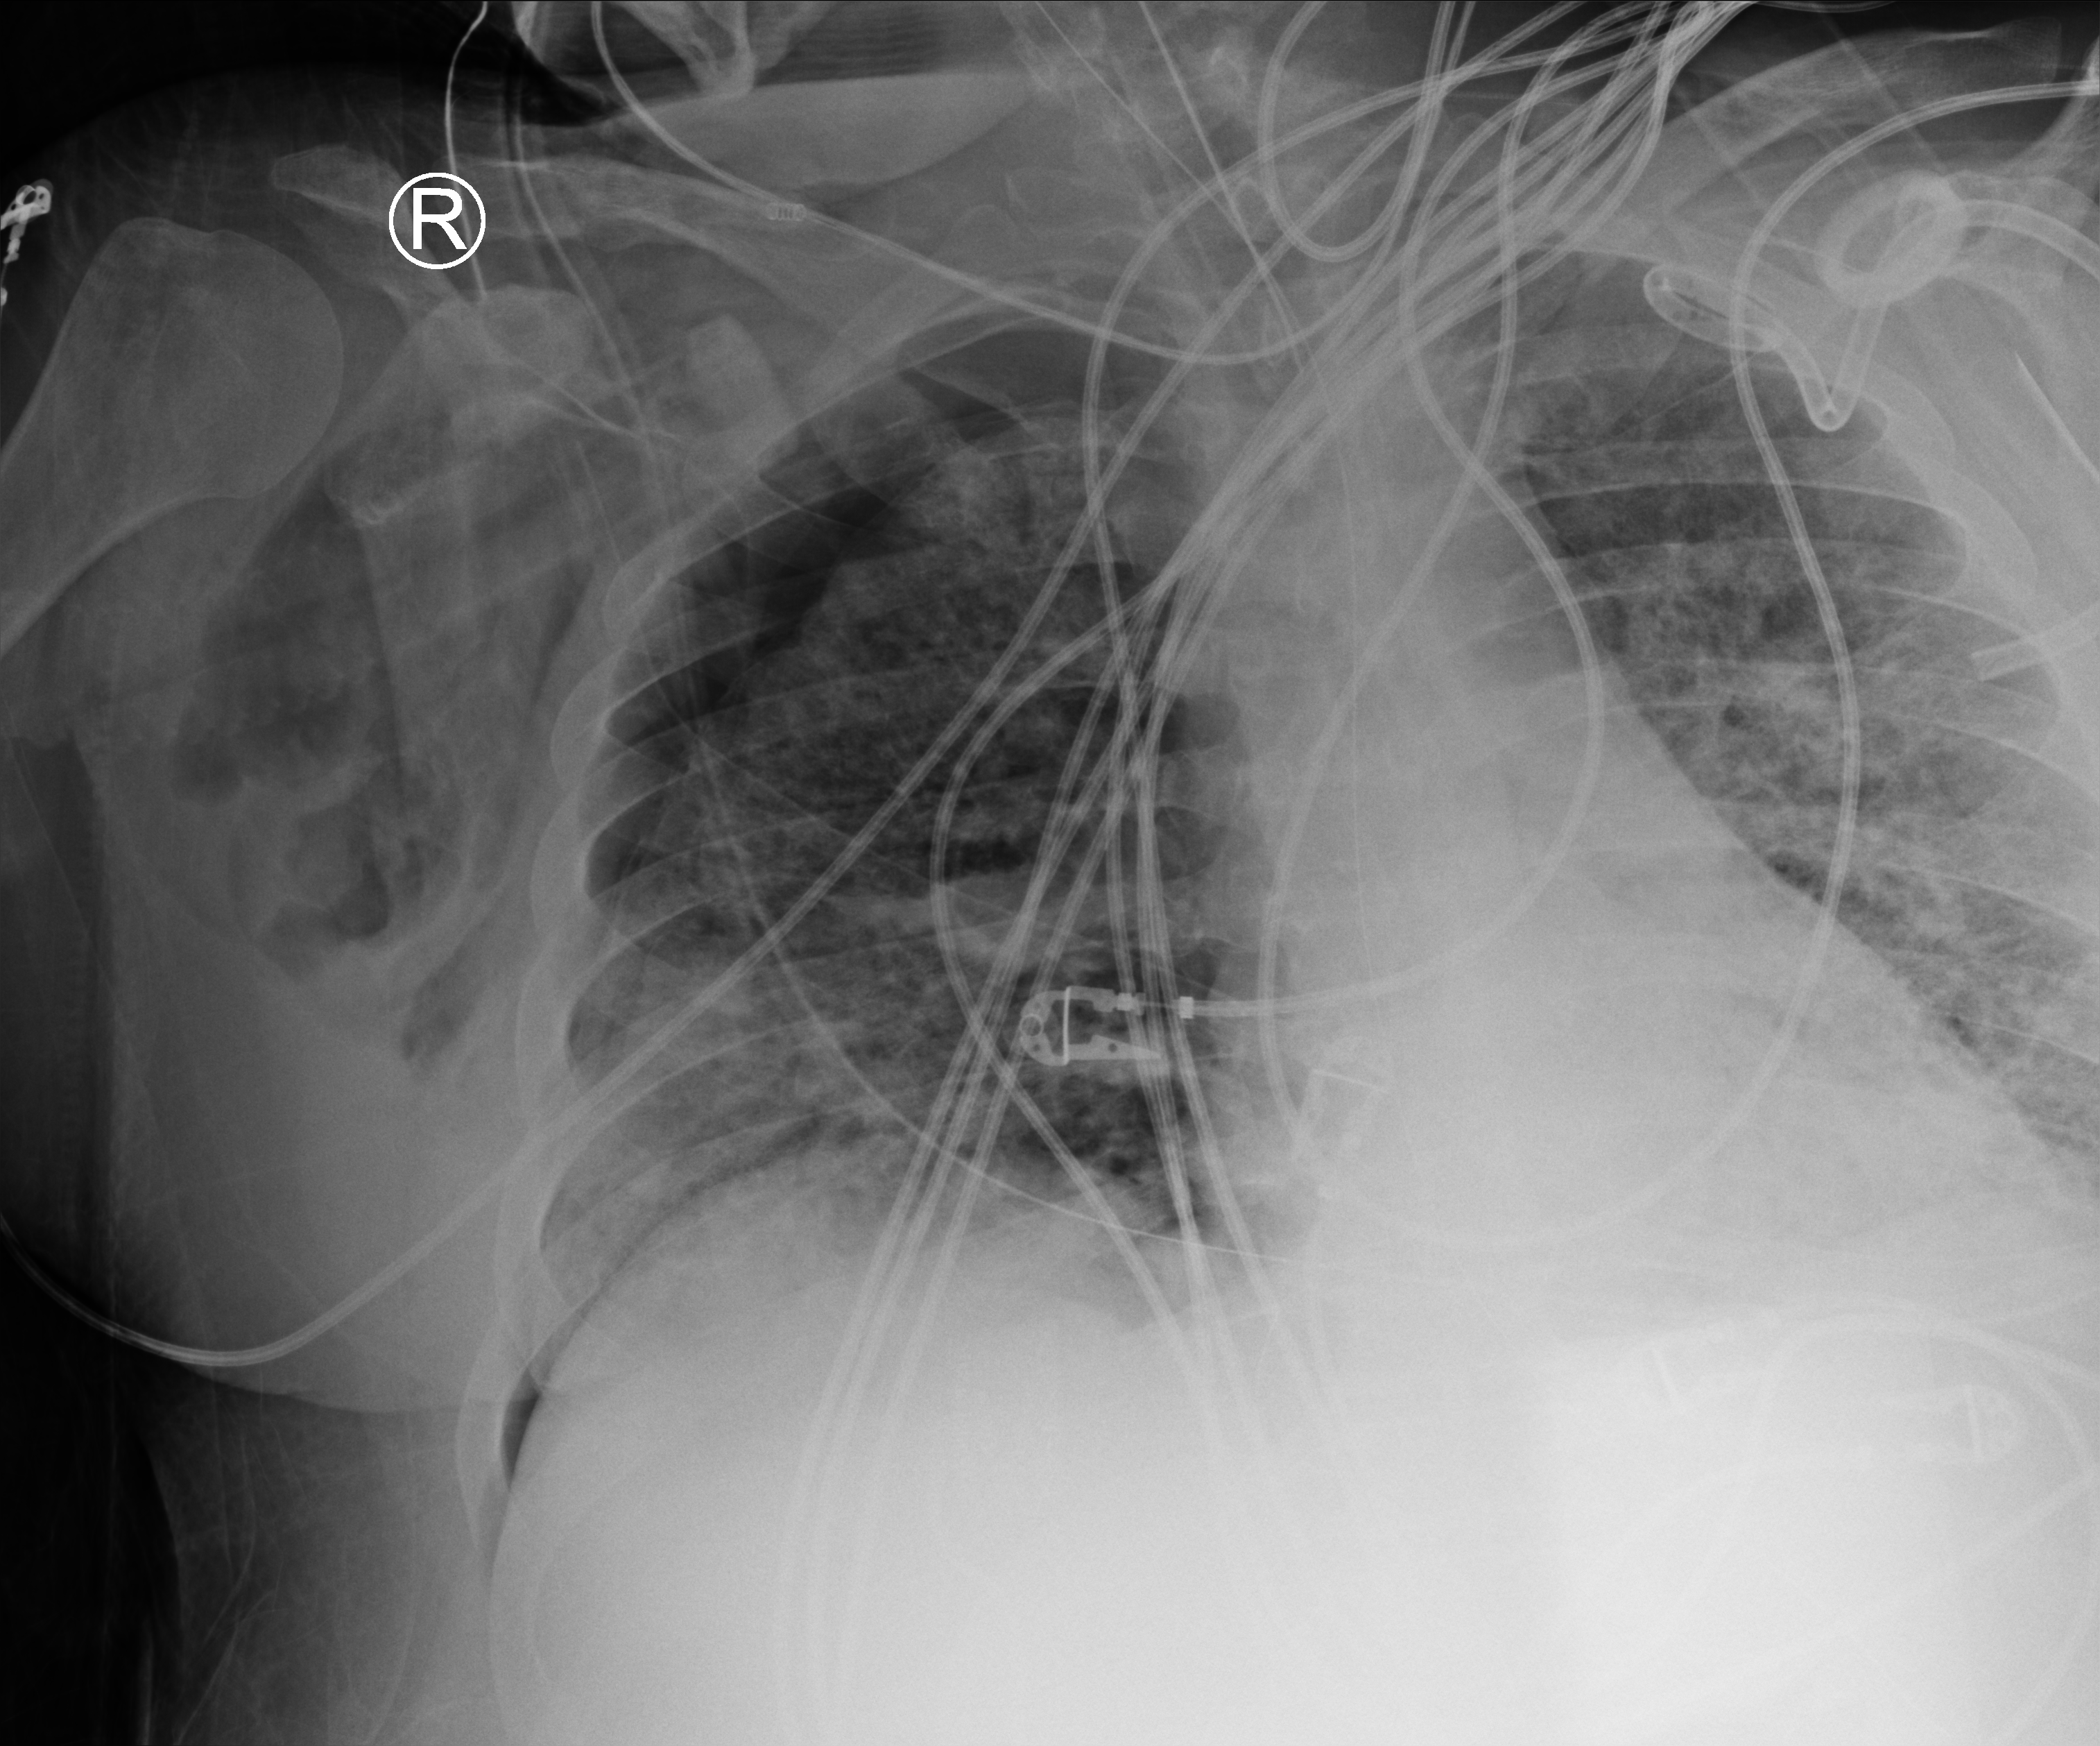
Chest X-ray (portable); anteroposterior (AP) projection. Adult patient hospitalised with COVID-19, age 18–59 years.
Hospital-stay facts (about this admission, not read from this image; timing relative to this image not recorded): length of hospital stay: 31 days.